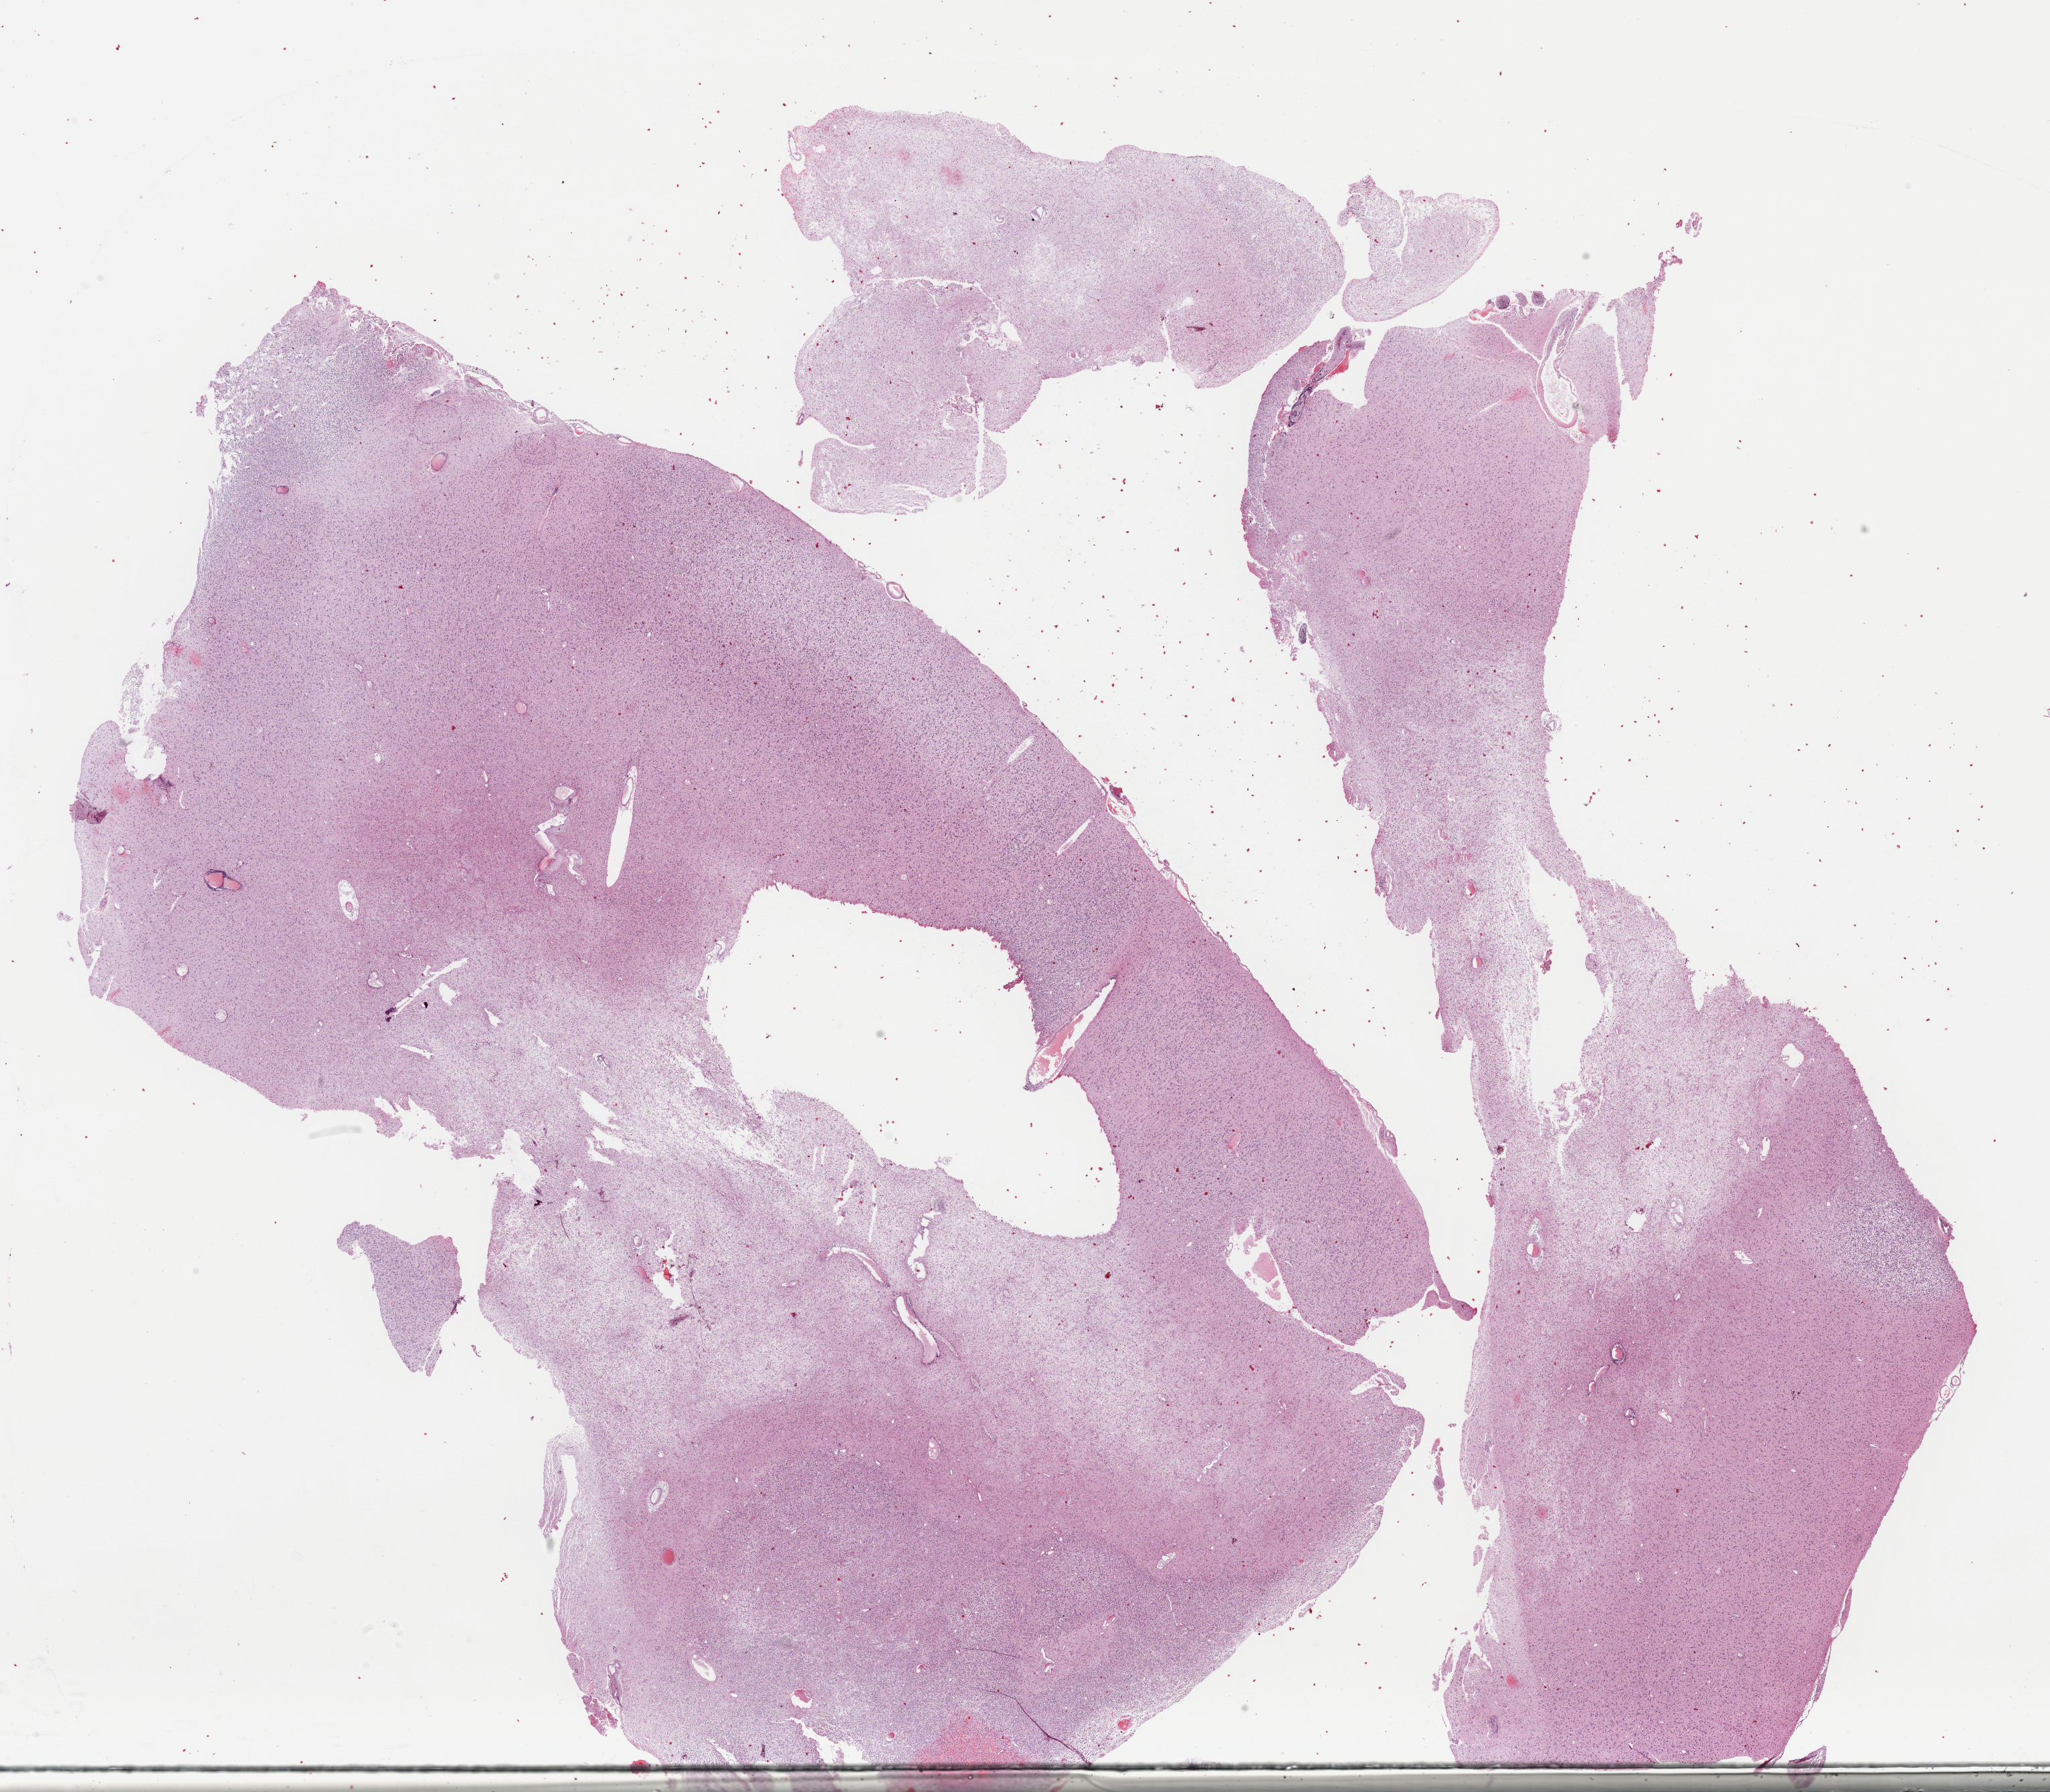
Whole-slide histology image, H&E-stained — shown as a low-resolution overview of the whole scanned area (about 24.2 x 21.1 mm, from a 40x scan); FFPE section; sample: primary tumour, brain. Male patient; age at initial diagnosis 54 years. Histologic grade: G2 (moderately differentiated).
Diagnosis: Oligodendroglioma, NOS (cerebrum).